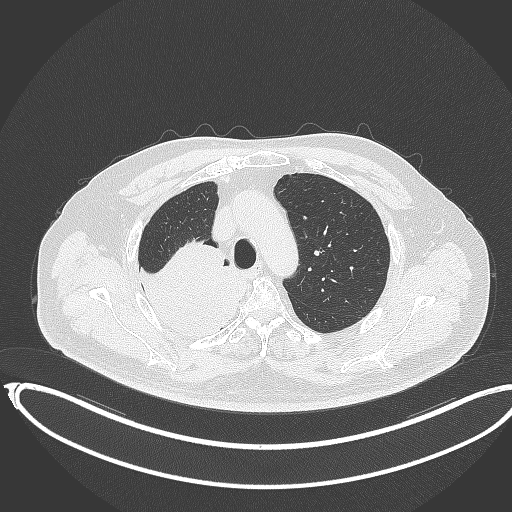
Chest CT, one axial slice; position 279 of 403 along the scan axis; reconstruction kernel B70f; 120 kVp; lung window (W 1500 / L -600 HU); 1 mm slice thickness; 512 × 512 image matrix, field of view 436 × 436 mm. Male patient, age 68 years. Case-level facts recorded for this patient, not image findings: clinical TNM (as recorded): T2a N0 M0.
Outlined on this slice (rectangle marked by the reading radiologist):
- lung tumour (recorded histology: adenocarcinoma): box from (x=133, y=238) to (x=246, y=340) px